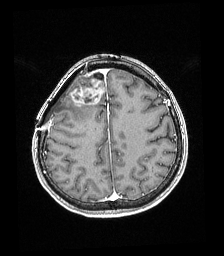
Brain MRI from a brain-tumour surgery series, one axial slice; position 62 of 192 along the scan axis; T1-weighted post-contrast; 224 × 256 image matrix, field of view 219 × 250 mm. Case-level facts recorded for this patient, not image findings: histopathology: Astrocytoma; WHO grade: 4; IDH mutation: yes.
Outlined on this slice (expert manual segmentation):
- tumour: bounding box (x1, y1, x2, y2) in pixels: (69, 80, 105, 106)